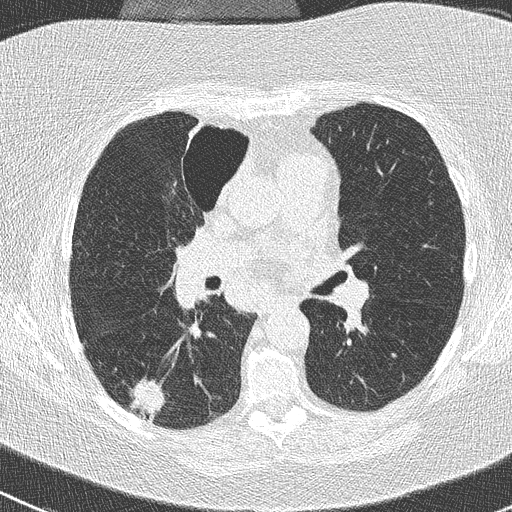
Chest CT (low-dose screening protocol), one axial image. Baseline screening round. Lung window (W 1500 / L -600 HU). 120 kVp. Slice 117 of 261 in the series. Female participant, aged 74 years at enrolment.
Expert reader's lesion annotation, bounding box <119,375,174,429> (left, top, right, bottom; pixels). The screening reader recorded 3 non-calcified nodules or masses ≥4 mm on this exam (right lower lobe, right upper lobe, left lower lobe); which of them this box marks is not recorded. Official screen result: positive, change unspecified: nodule(s) >= 4 mm or enlarging nodule(s), mass(es), or other non-specific abnormalities suspicious for lung cancer. Later outcome: lung cancer diagnosed 16 days after this screen — non-small cell carcinoma, right lower lobe, poorly differentiated (G3), stage IIIA (AJCC 6th edition), 28 mm at pathology.